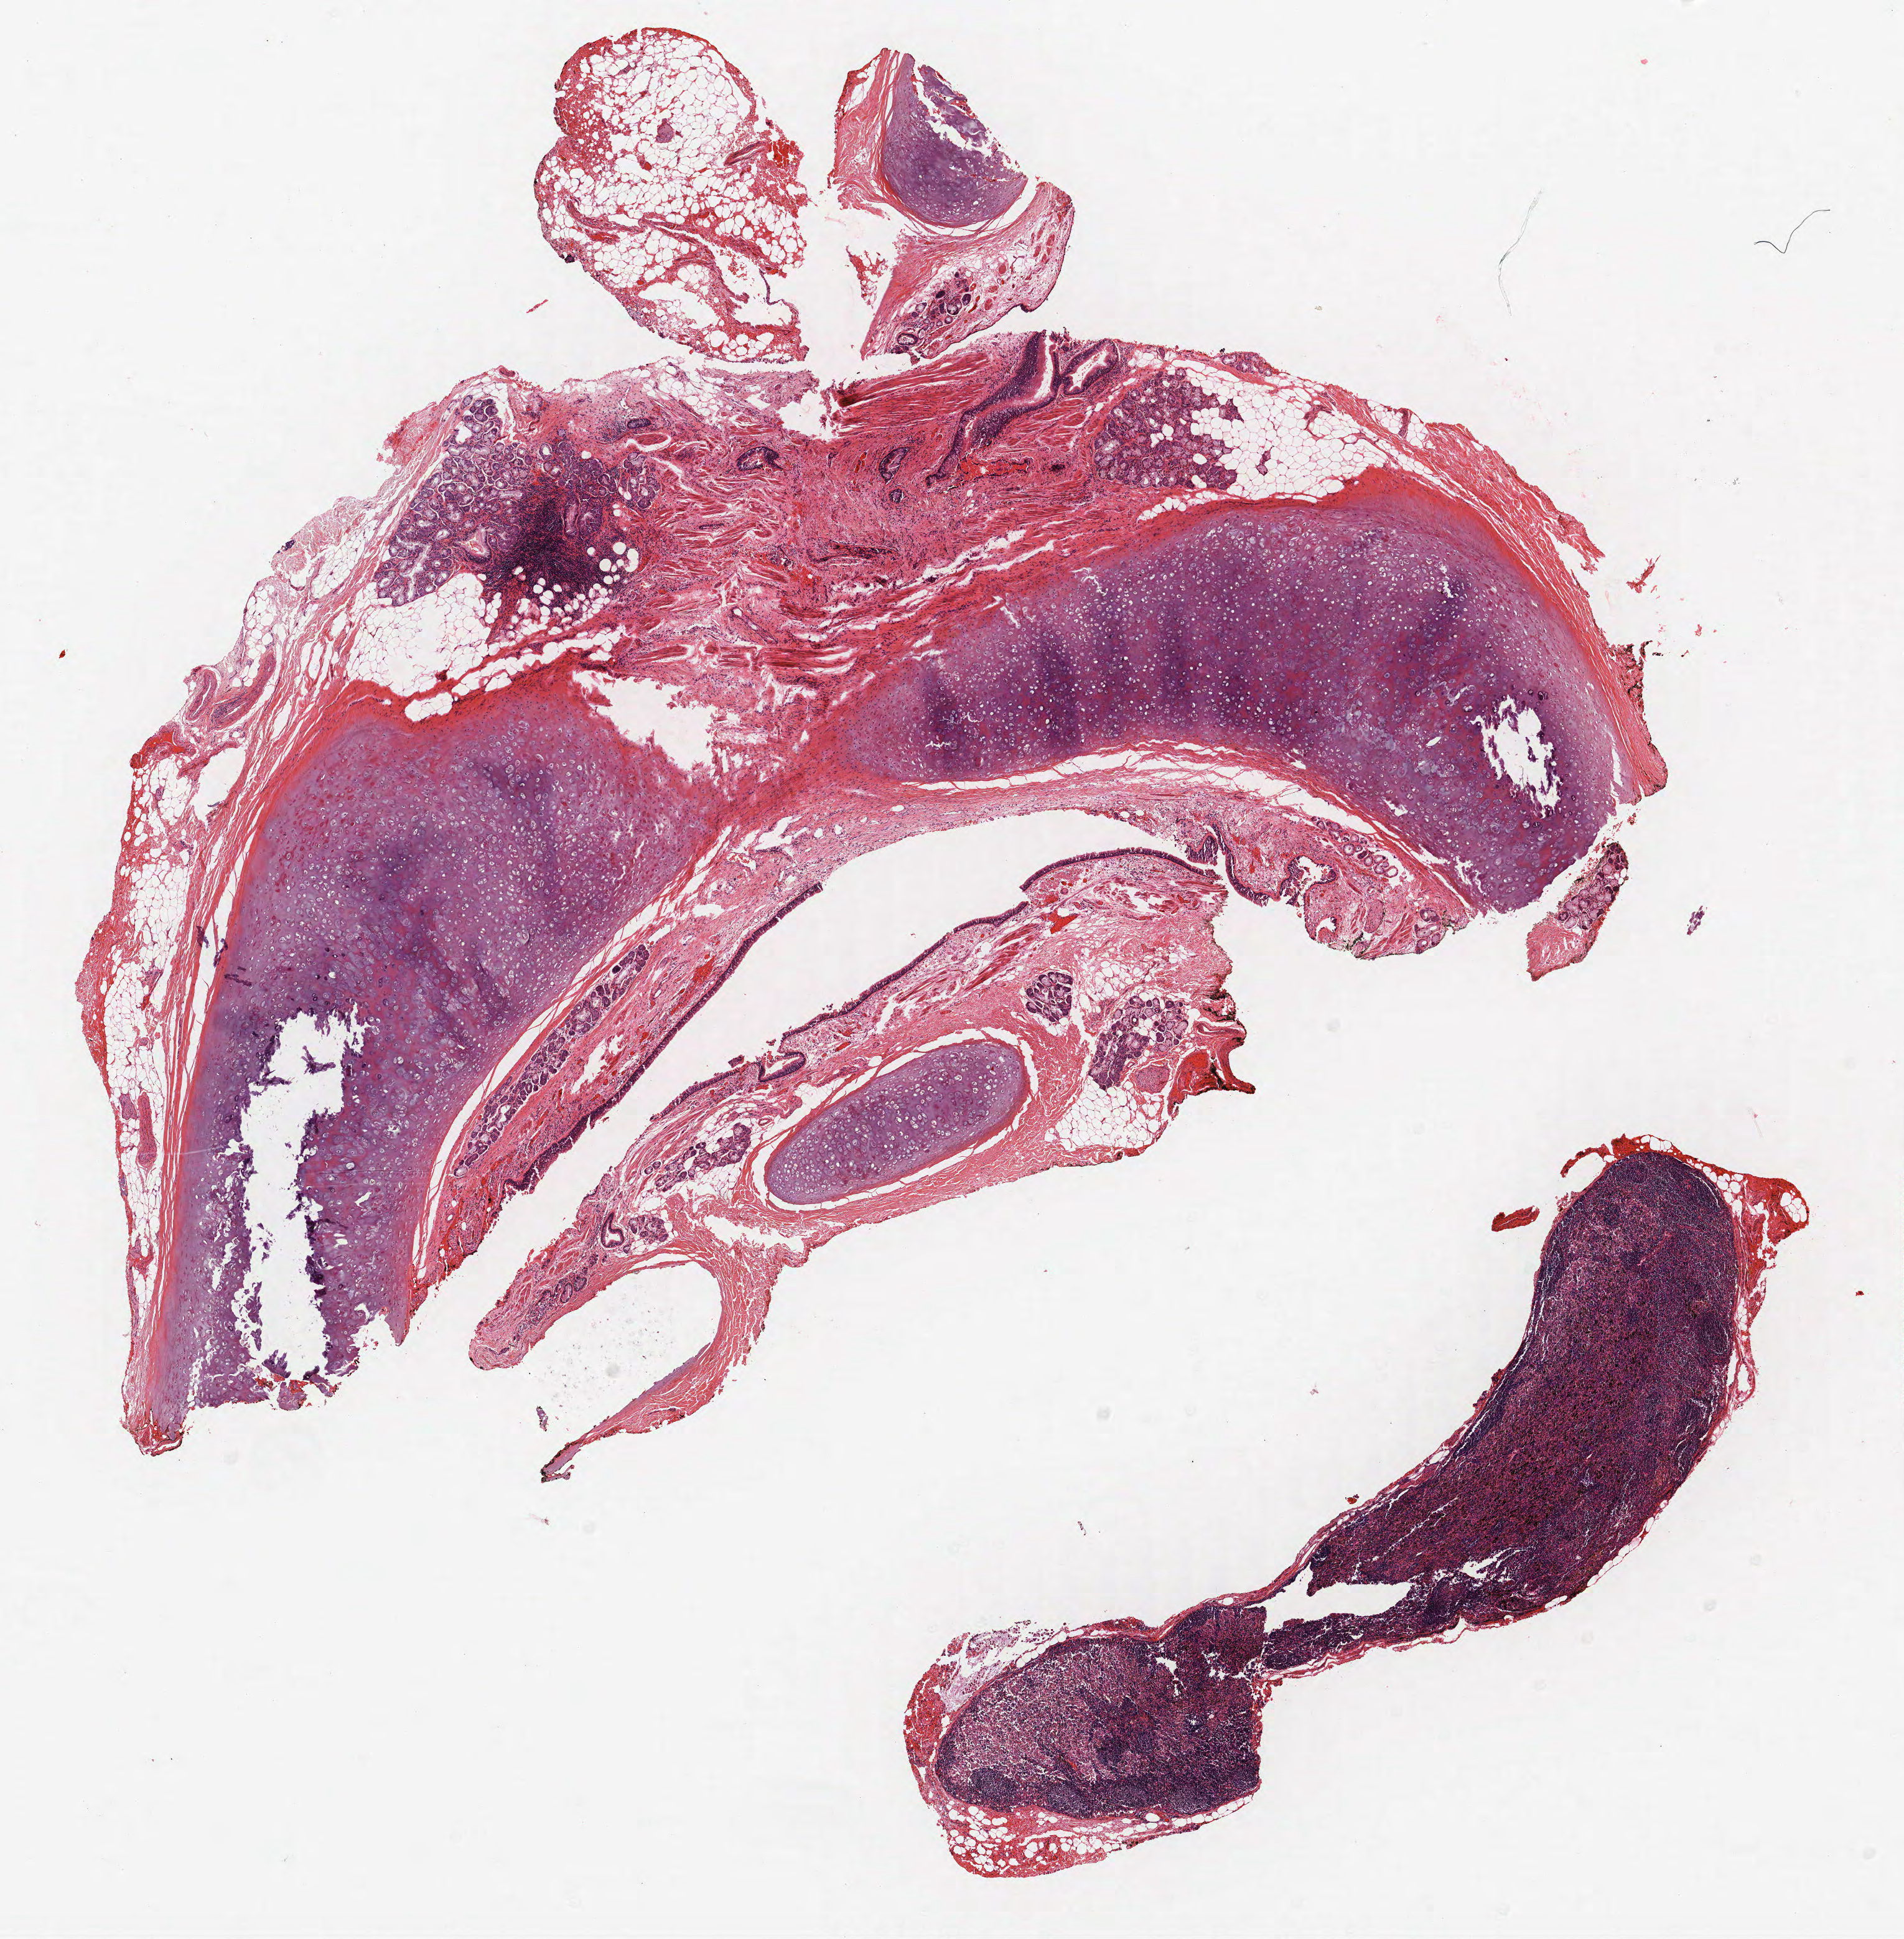
Whole-slide histology image, Hematoxylin and eosin (H&E) stained — a low-resolution overview of the entire scanned area, about 12.2 x 12.5 mm (acquisition: 40x scan); FFPE section; lung. Male, age 60 at enrolment. Current smoker at enrolment.
Participant's lung-cancer diagnosis: Papillary adenocarcinoma, NOS (ICD-O-3 8260/3).